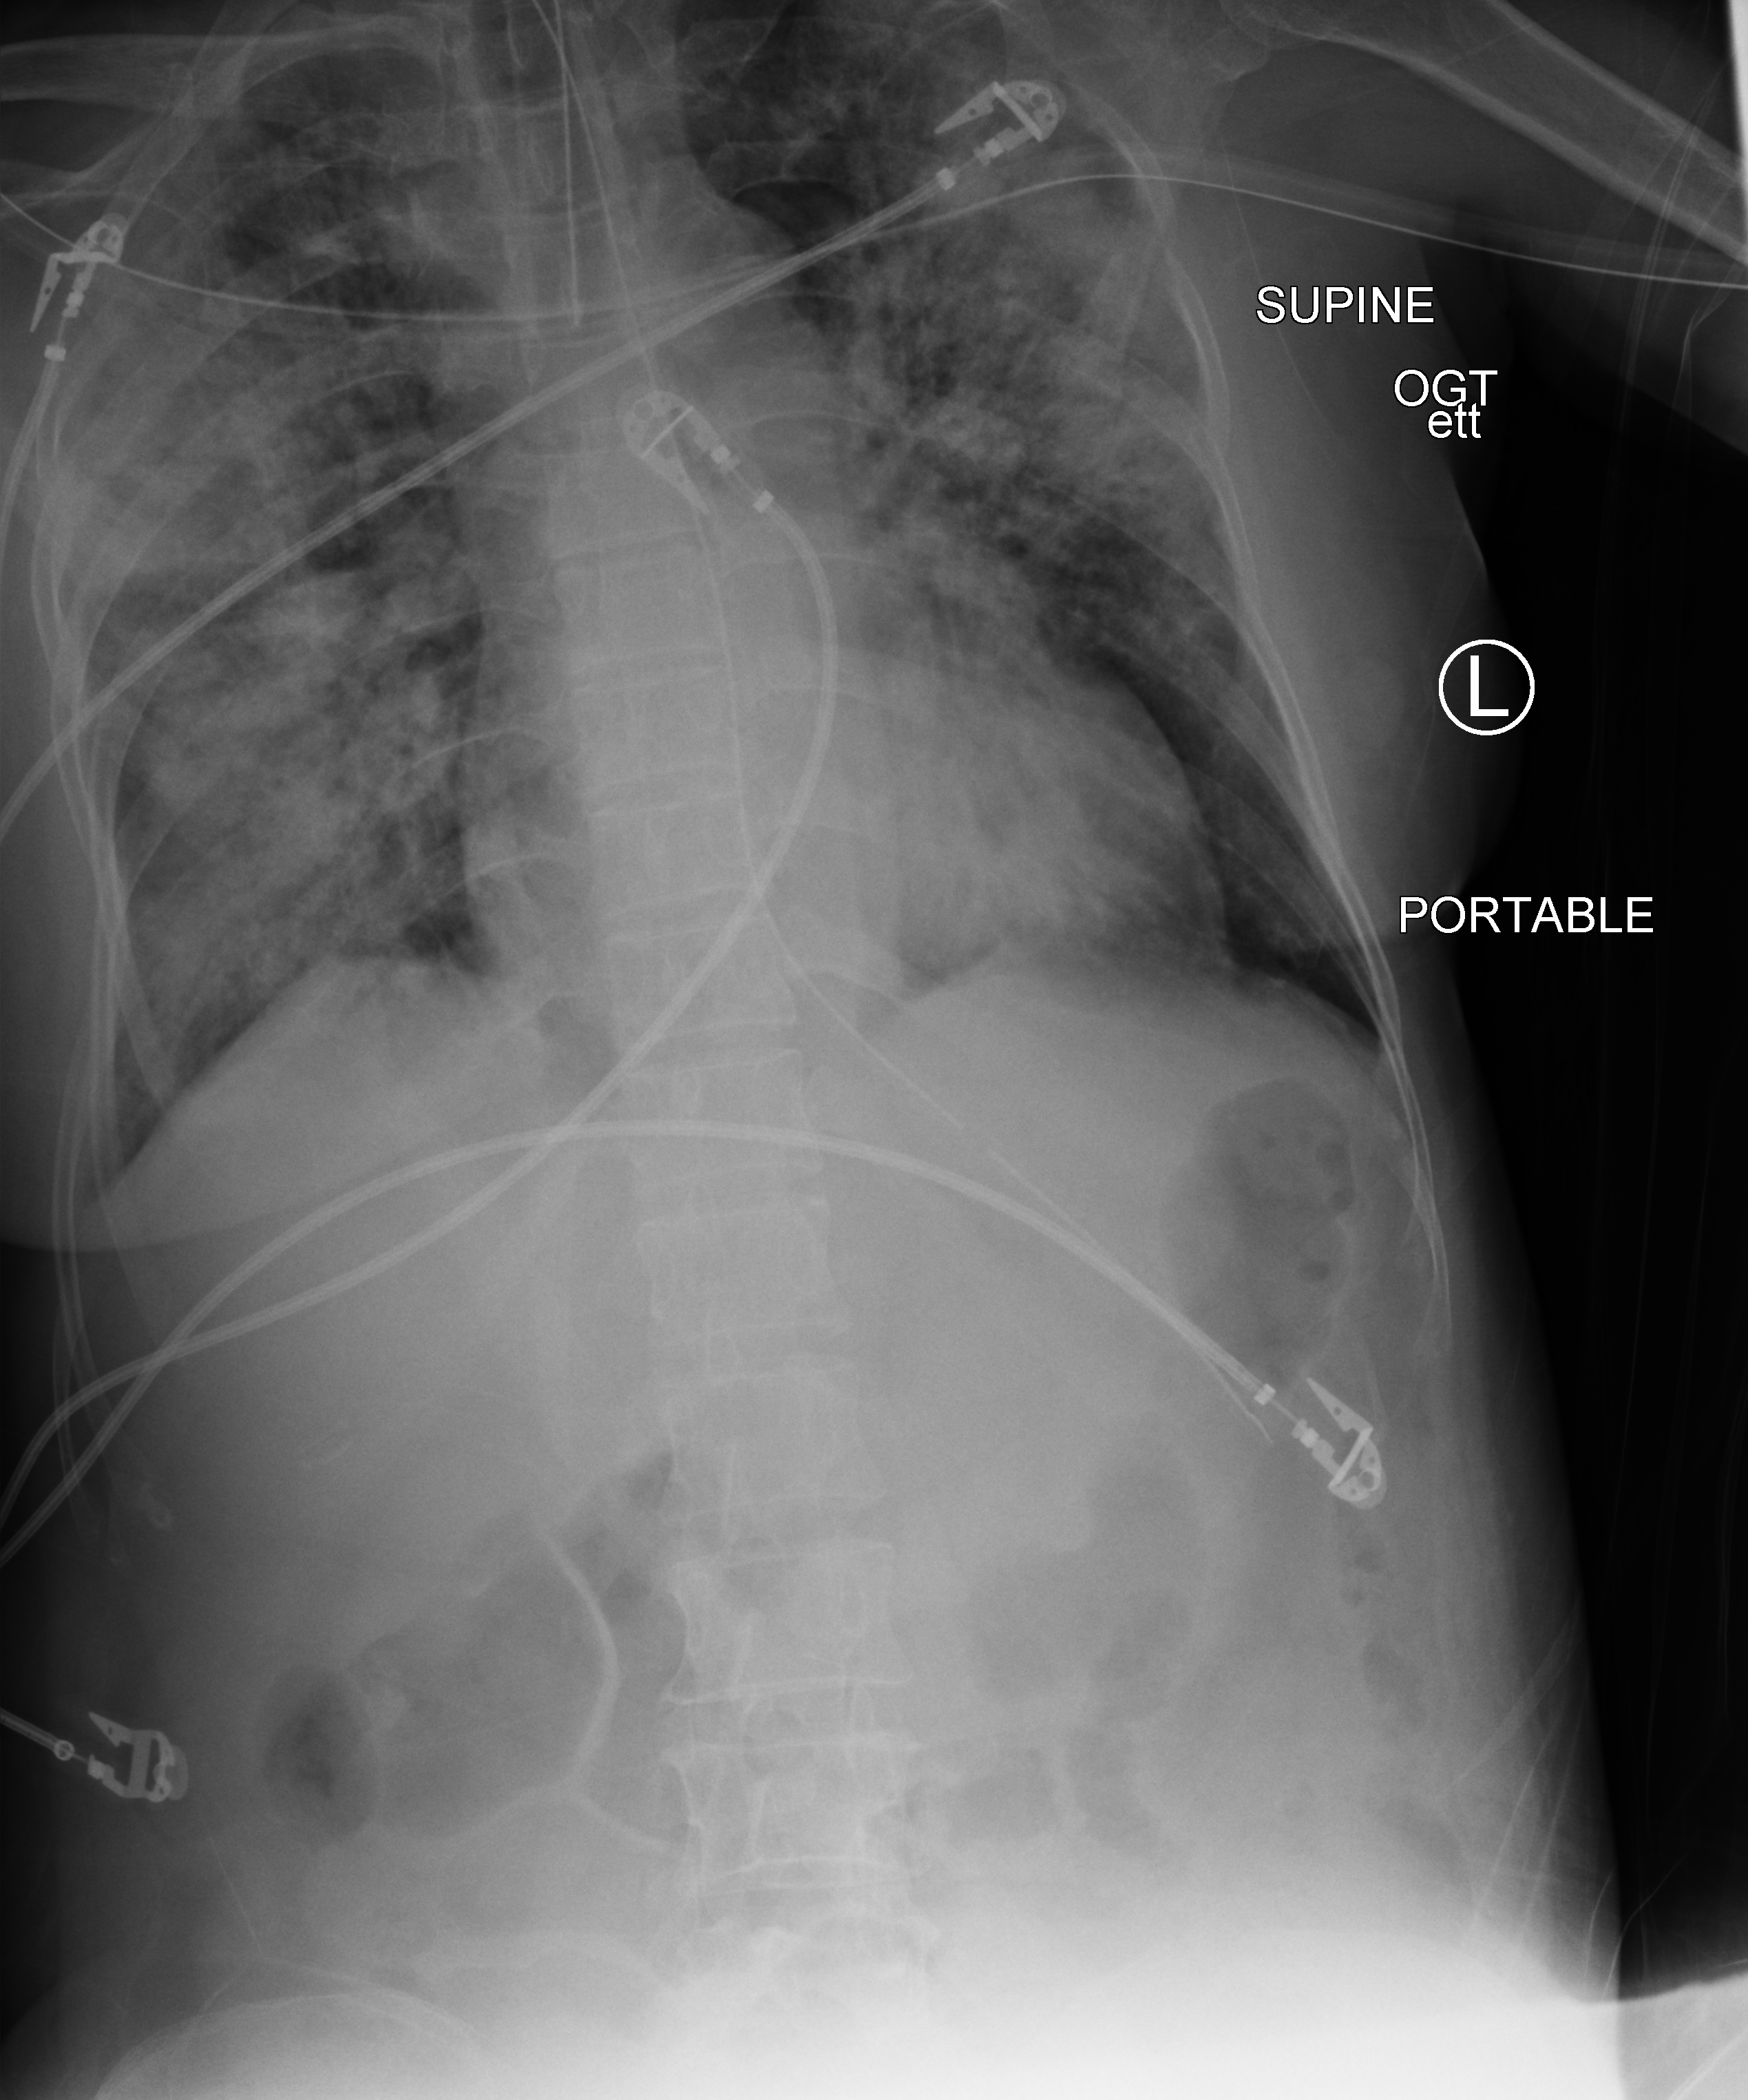
Portable chest radiograph, anteroposterior (AP) projection. Patient hospitalised with COVID-19; female, aged 60–74 years.
From the hospital-stay record, not from the radiograph (when in the stay this image was taken is not recorded):
- COPD (admission record): no
- admitted to intensive care during this hospital stay: yes
- mechanically ventilated during this hospital stay: yes